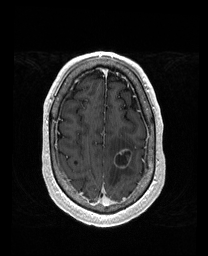
Brain MRI from a brain-tumour surgery series, one axial slice. Slice 142 of 192 in the series (ordered by position). T1-weighted post-contrast. 1 mm slice thickness. 208 × 256 image matrix, field of view 211 × 260 mm. From the clinical record (not read from this slice): histopathology: Metastatic Carcinoma from Lung Adenocarcinoma.
Annotated regions visible in this slice (outlined manually by an expert reader):
- tumour: bounding box <114,150,132,168> (left, top, right, bottom; pixels)